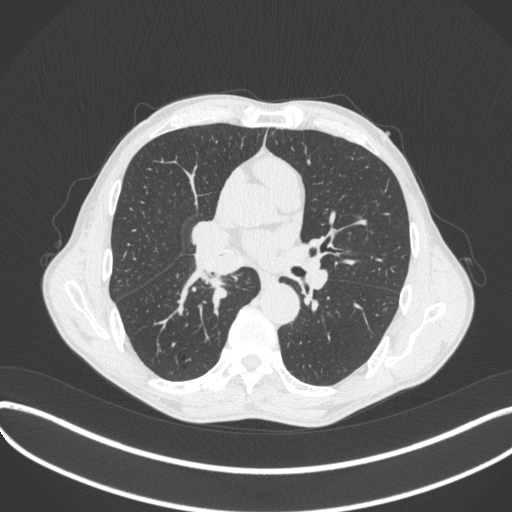
Chest CT, one axial slice; slice 234 of 481 in the series (ordered by position); 120 kVp; lung window (W 1500 / L -600 HU); 1 mm slice thickness; 512 × 512 image matrix, field of view 400 × 400 mm. Male patient, age 65 years. From the clinical record (not read from this slice): clinical TNM (as recorded): T2a N0 M0; histopathological grade: G2.
Annotated regions visible in this slice (bounding box drawn by a radiologist):
- lung tumour (recorded histology: squamous cell carcinoma): bounding box [x1, y1, x2, y2] px = [185, 240, 240, 307]